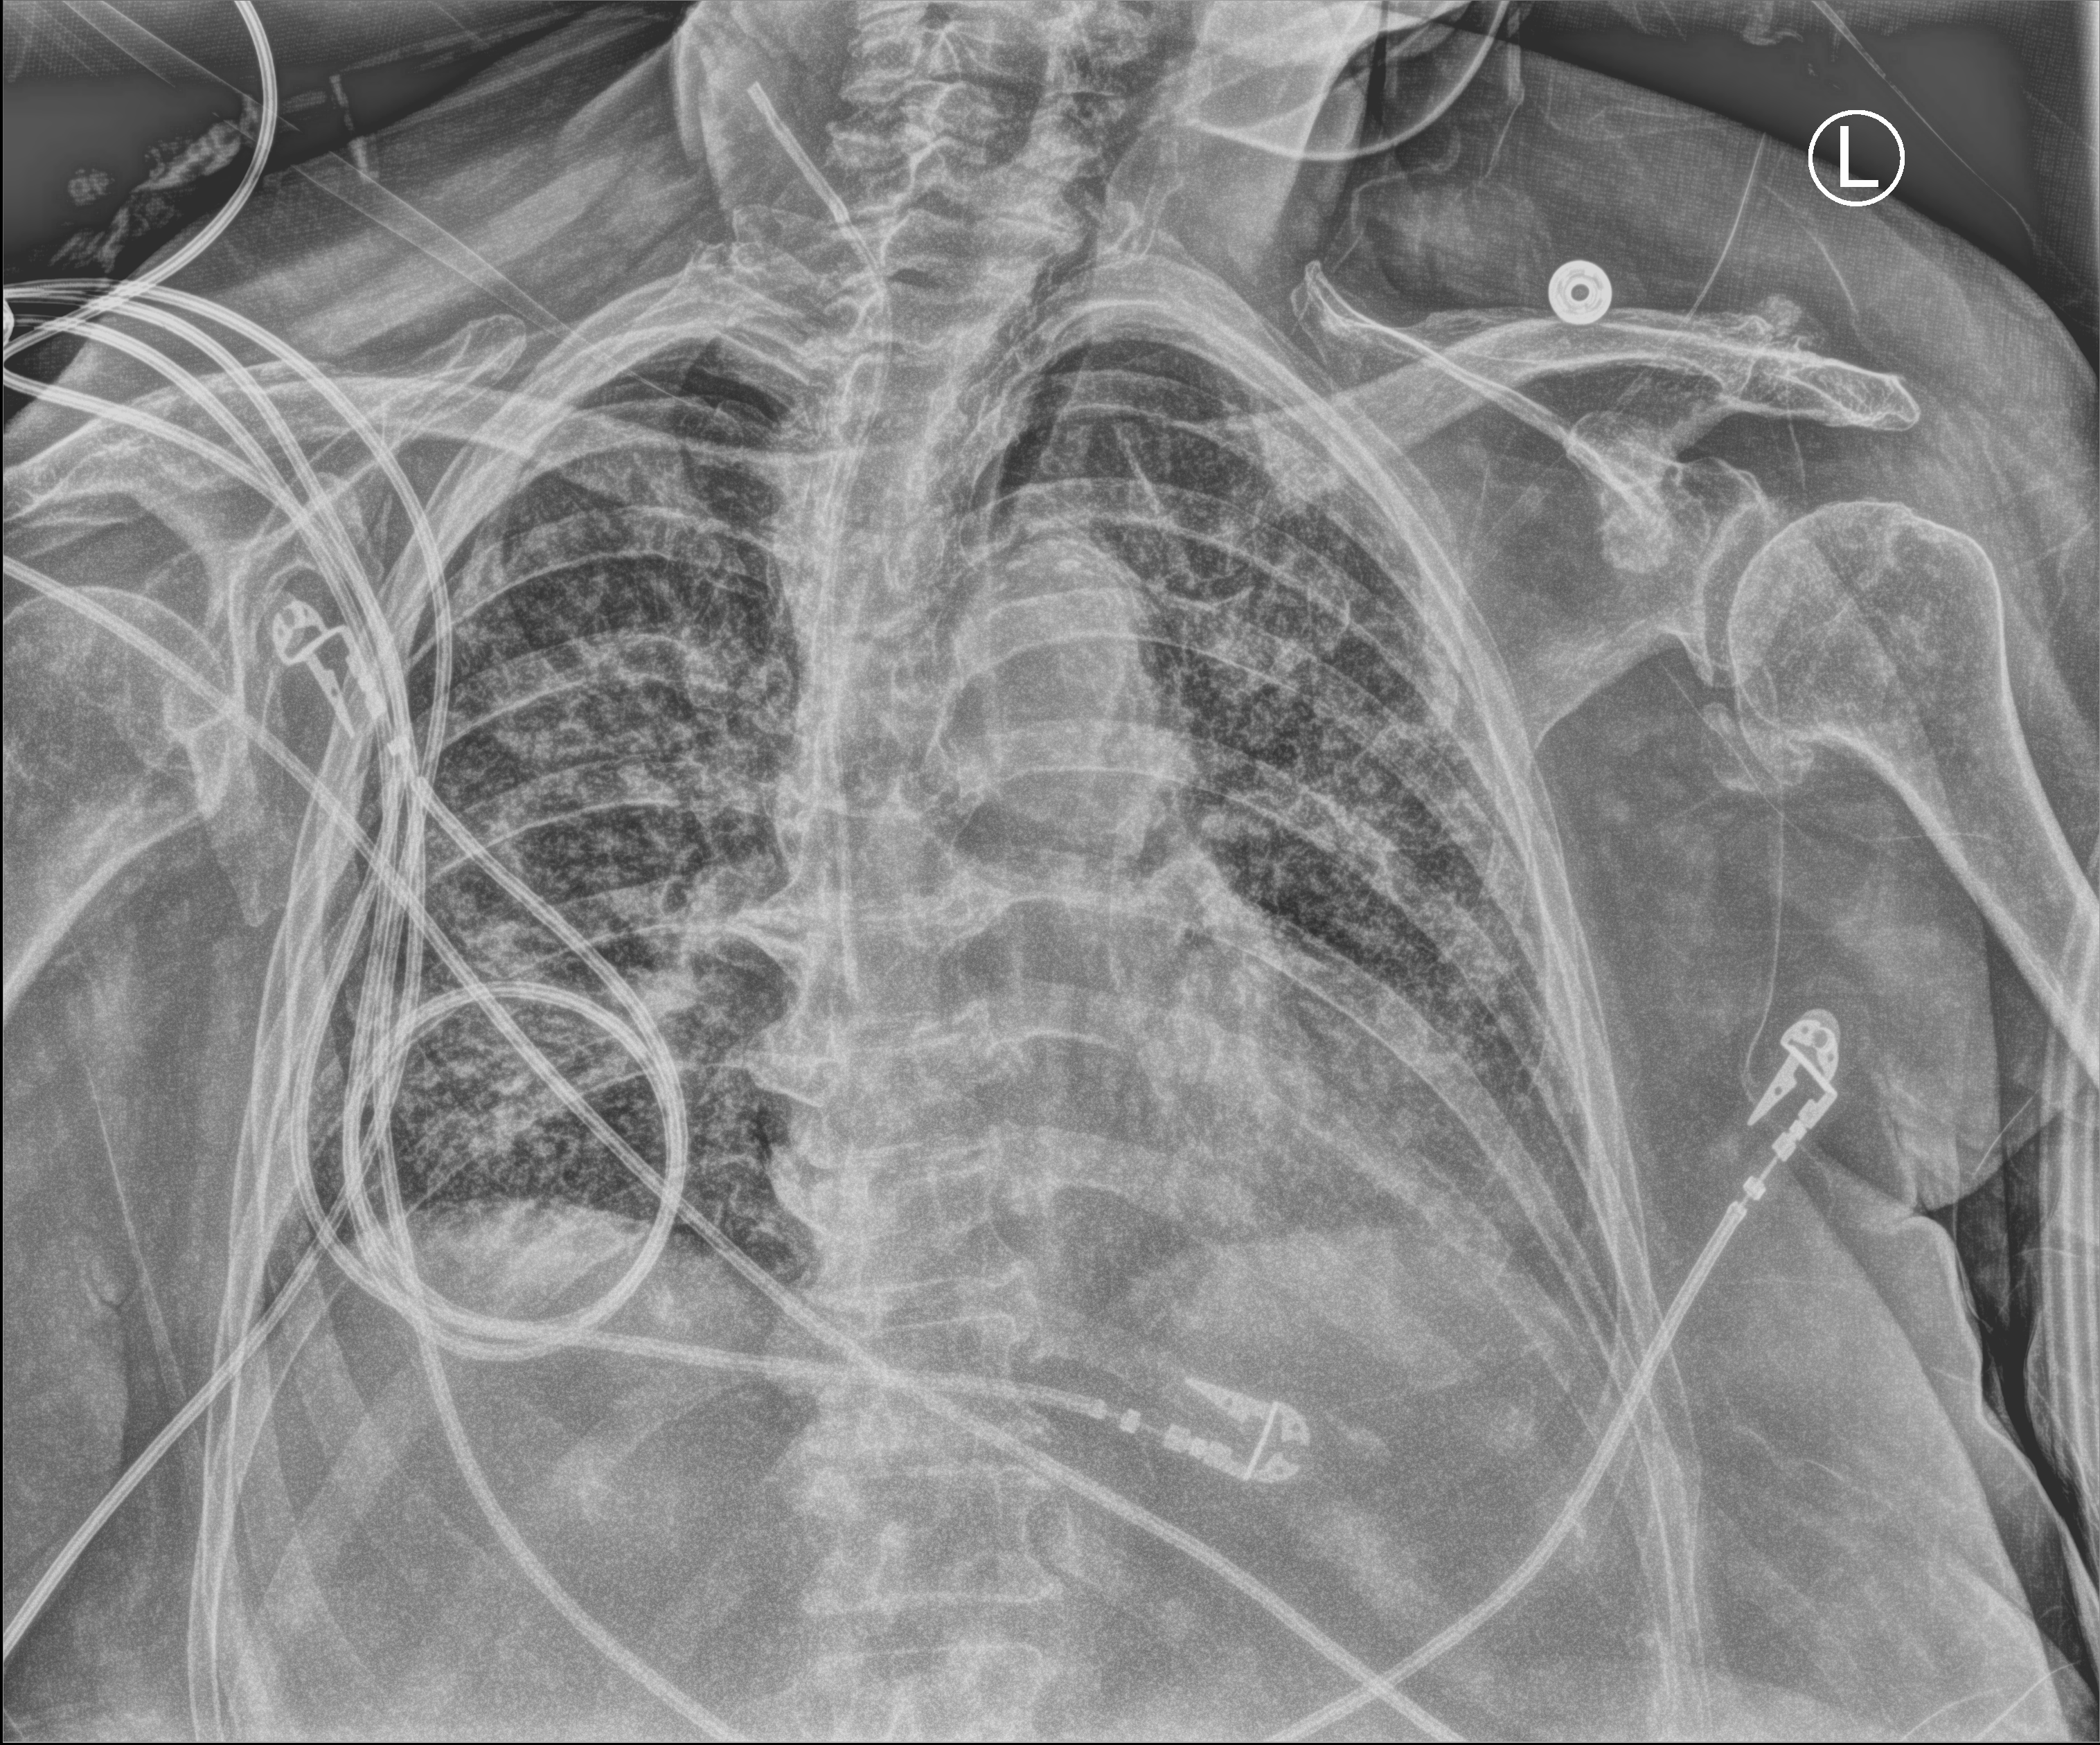
Chest X-ray (portable), anteroposterior (AP) projection. Patient hospitalised with COVID-19; female, aged 75–90 years.
Hospital-stay facts (about this admission, not read from this image; timing relative to this image not recorded): diabetes (admission record): no; mechanically ventilated during this hospital stay: yes; other chronic lung disease (admission record): no.